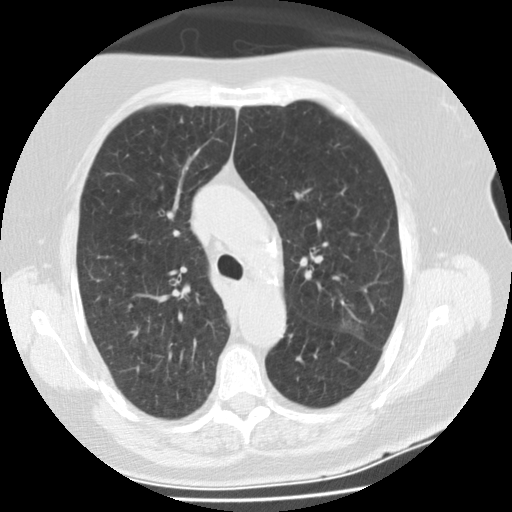
Low-dose screening chest CT, axial slice, second annual screen, lung window (W 1500 / L -600 HU), 120 kVp, slice 86 of 297 in the series. Female, age 74 years at enrolment. Former smoker at enrolment.
Expert reader's lesion annotation, bounding box (x1, y1, x2, y2) in pixels: (325, 301, 388, 359). The screening reader recorded 3 non-calcified nodules or masses ≥4 mm on this exam (right lower lobe, left upper lobe, left upper lobe); which of them this box marks is not recorded. Official screen result: positive, other. Lung cancer was diagnosed 68 days after this screen: bronchiolo-alveolar adenocarcinoma, NOS, left upper lobe, stage IA (AJCC 6th edition), 20 mm at pathology.